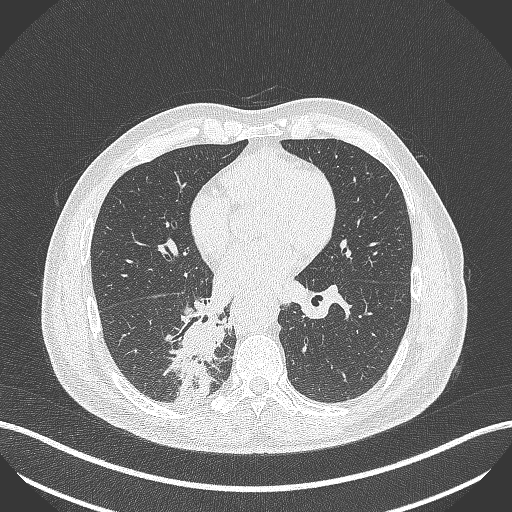
Chest CT, one axial slice; position 218 of 451 along the scan axis; reconstruction kernel B70f; 100 kVp; lung window (W 1500 / L -600 HU); 1 mm slice thickness; 512 × 512 image matrix. Male patient, age 61 years. Case-level facts recorded for this patient, not image findings: clinical TNM (as recorded): T1 N0 M0; histopathological grade: G3.
Outlined on this slice (rectangle marked by the reading radiologist):
- lung tumour (recorded histology: small cell carcinoma): bounding box <170,312,226,415> (left, top, right, bottom; pixels)